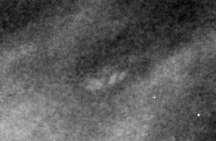
Region of interest cut from a scanned film mammogram (one marked finding); left breast; MLO view; BI-RADS breast density category 4 (scale 1–4).
- Calcifications, morphology pleomorphic, distribution linear; BI-RADS assessment category 4; pathology (as recorded): malignant.